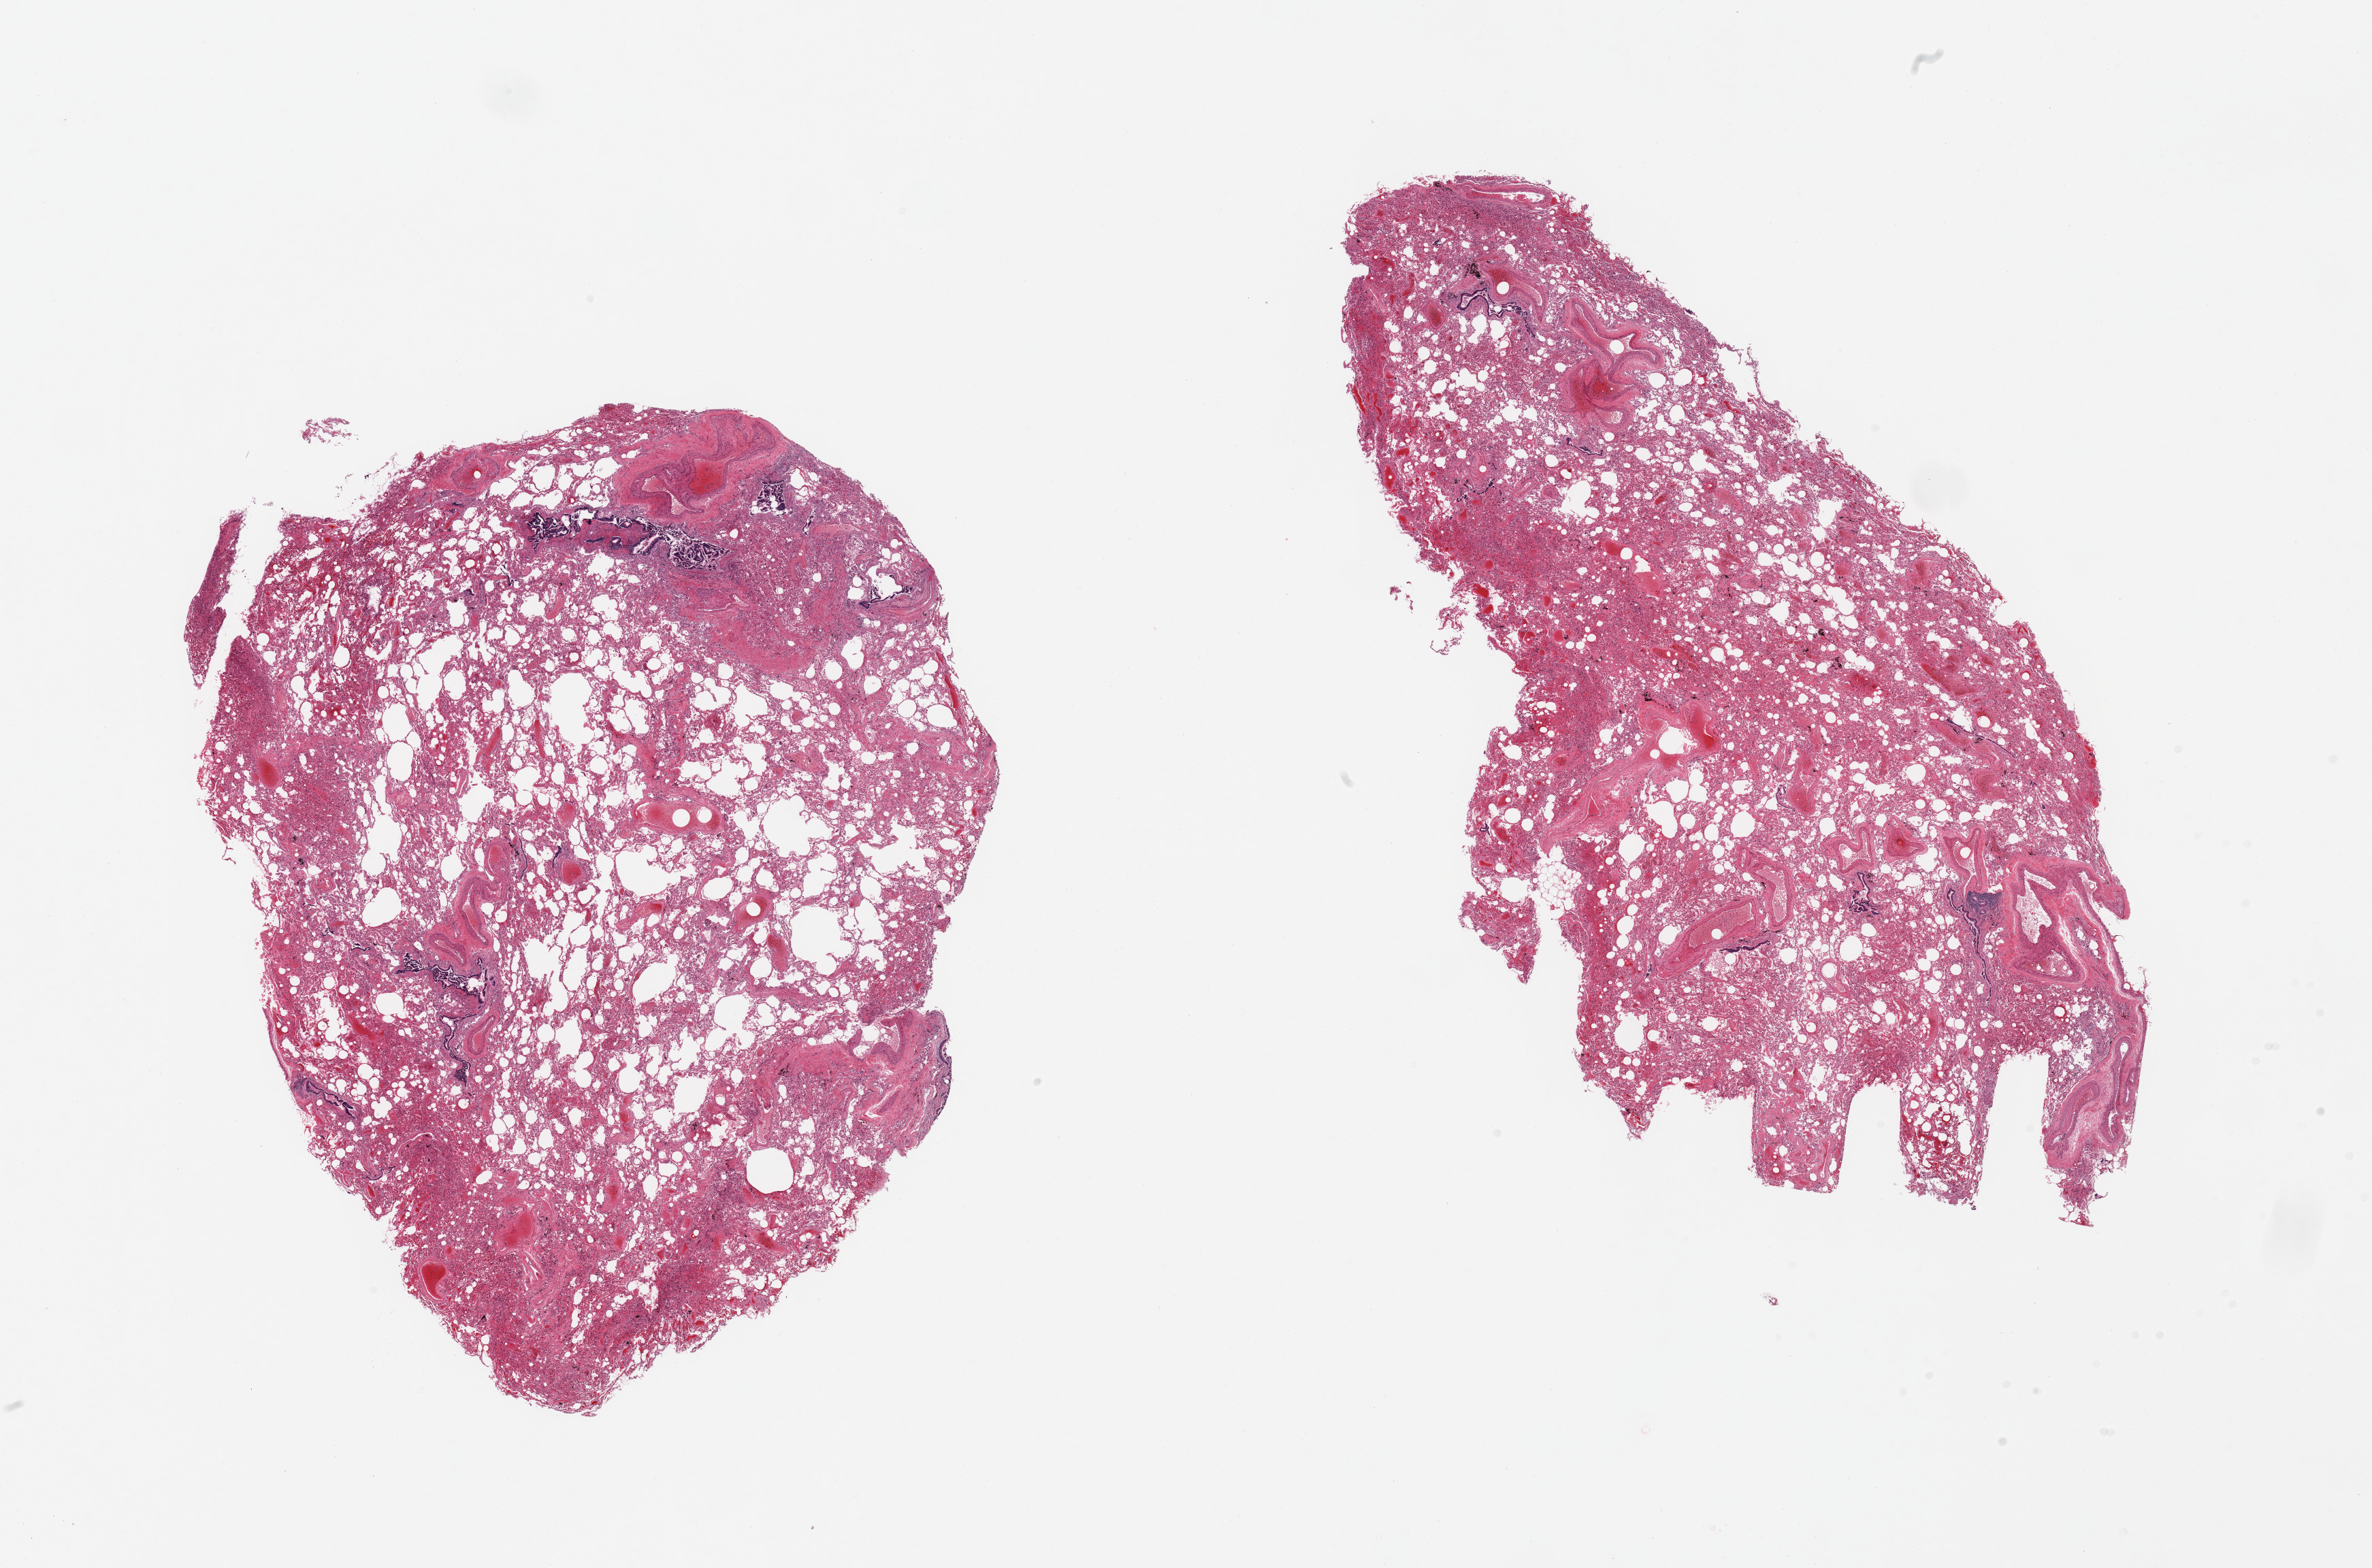
Whole-slide image, hematoxylin and eosin (H&E) stain — shown as a low-resolution overview of the whole scanned area (about 27.6 x 18.2 mm), PAXgene-fixed paraffin-embedded (PFPE) section, section of lung (target tissue), tissue donor sample. Male donor.
Reviewer comment on this tissue sample: 2 pieces patchy chronic, mildly active pneumonitis and atalectasis.